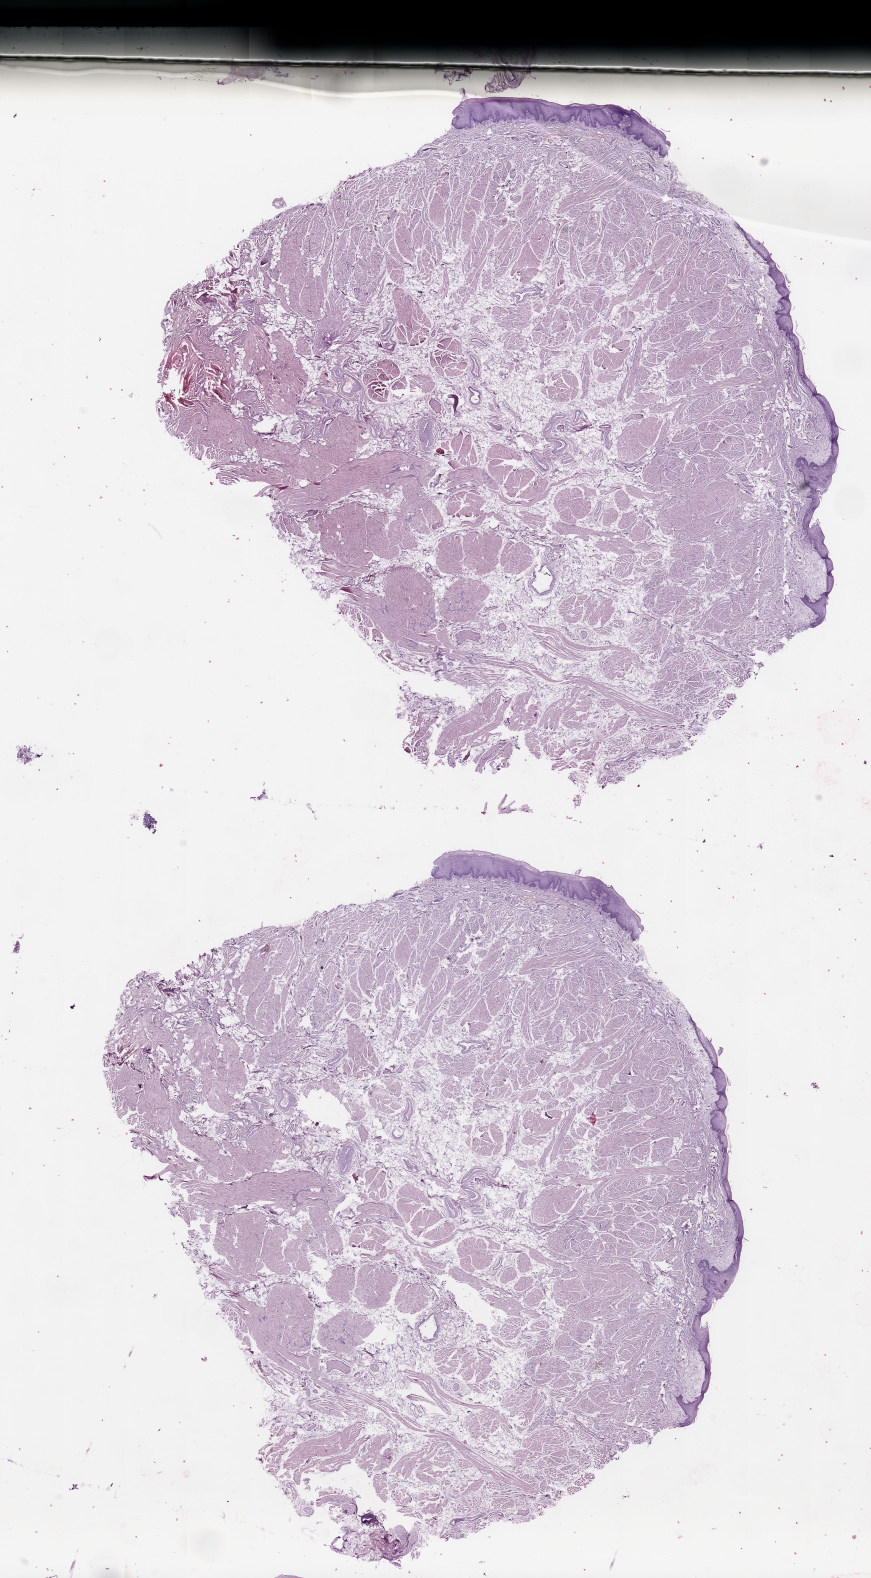
Whole-slide histology image, Hematoxylin and eosin (H&E) stained — low-resolution overview of the scanned area, about 13.8 x 25.0 mm (acquisition: 20x scan). Normal (non-tumour) tissue sample, sampled site: tongue. Male, 59 y/o.
* this section: normal (non-tumour) tissue from the same patient
* patient diagnosis: Squamous cell carcinoma, NOS (tongue, NOS)